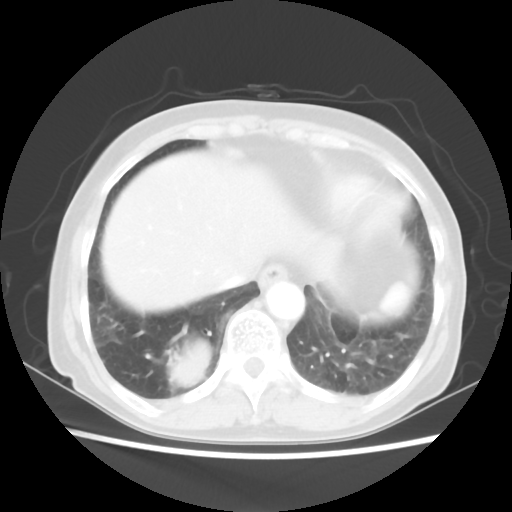
Chest CT, one axial slice. Position 16 of 56 along the scan axis. 120 kVp. Lung window (W 1500 / L -600 HU). 5 mm slice thickness. 512 × 512 image matrix. Female patient, age 66 years. From the clinical record (not read from this slice): clinical TNM (as recorded): T2 N3 M0.
Annotated regions visible in this slice (bounding box drawn by a radiologist):
- lung tumour (recorded histology: small cell carcinoma): bounding box (x1, y1, x2, y2) in pixels: (167, 338, 215, 386)